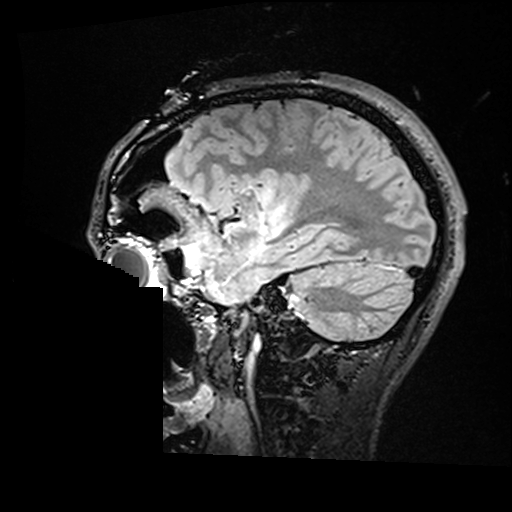
Brain MRI from a brain-tumour surgery series, one sagittal slice. Position 117 of 176 along the scan axis. T2 FLAIR. 1 mm slice thickness. 512 × 512 image matrix, field of view 250 × 250 mm. Case-level facts recorded for this patient, not image findings: histopathology: Astrocytoma; WHO grade: 2; IDH mutation: yes; tumour location: Right Insular.
Structures marked on this image (outlined manually by an expert reader):
- residual tumour: bounding box (x1, y1, x2, y2) in pixels: (260, 188, 285, 228)